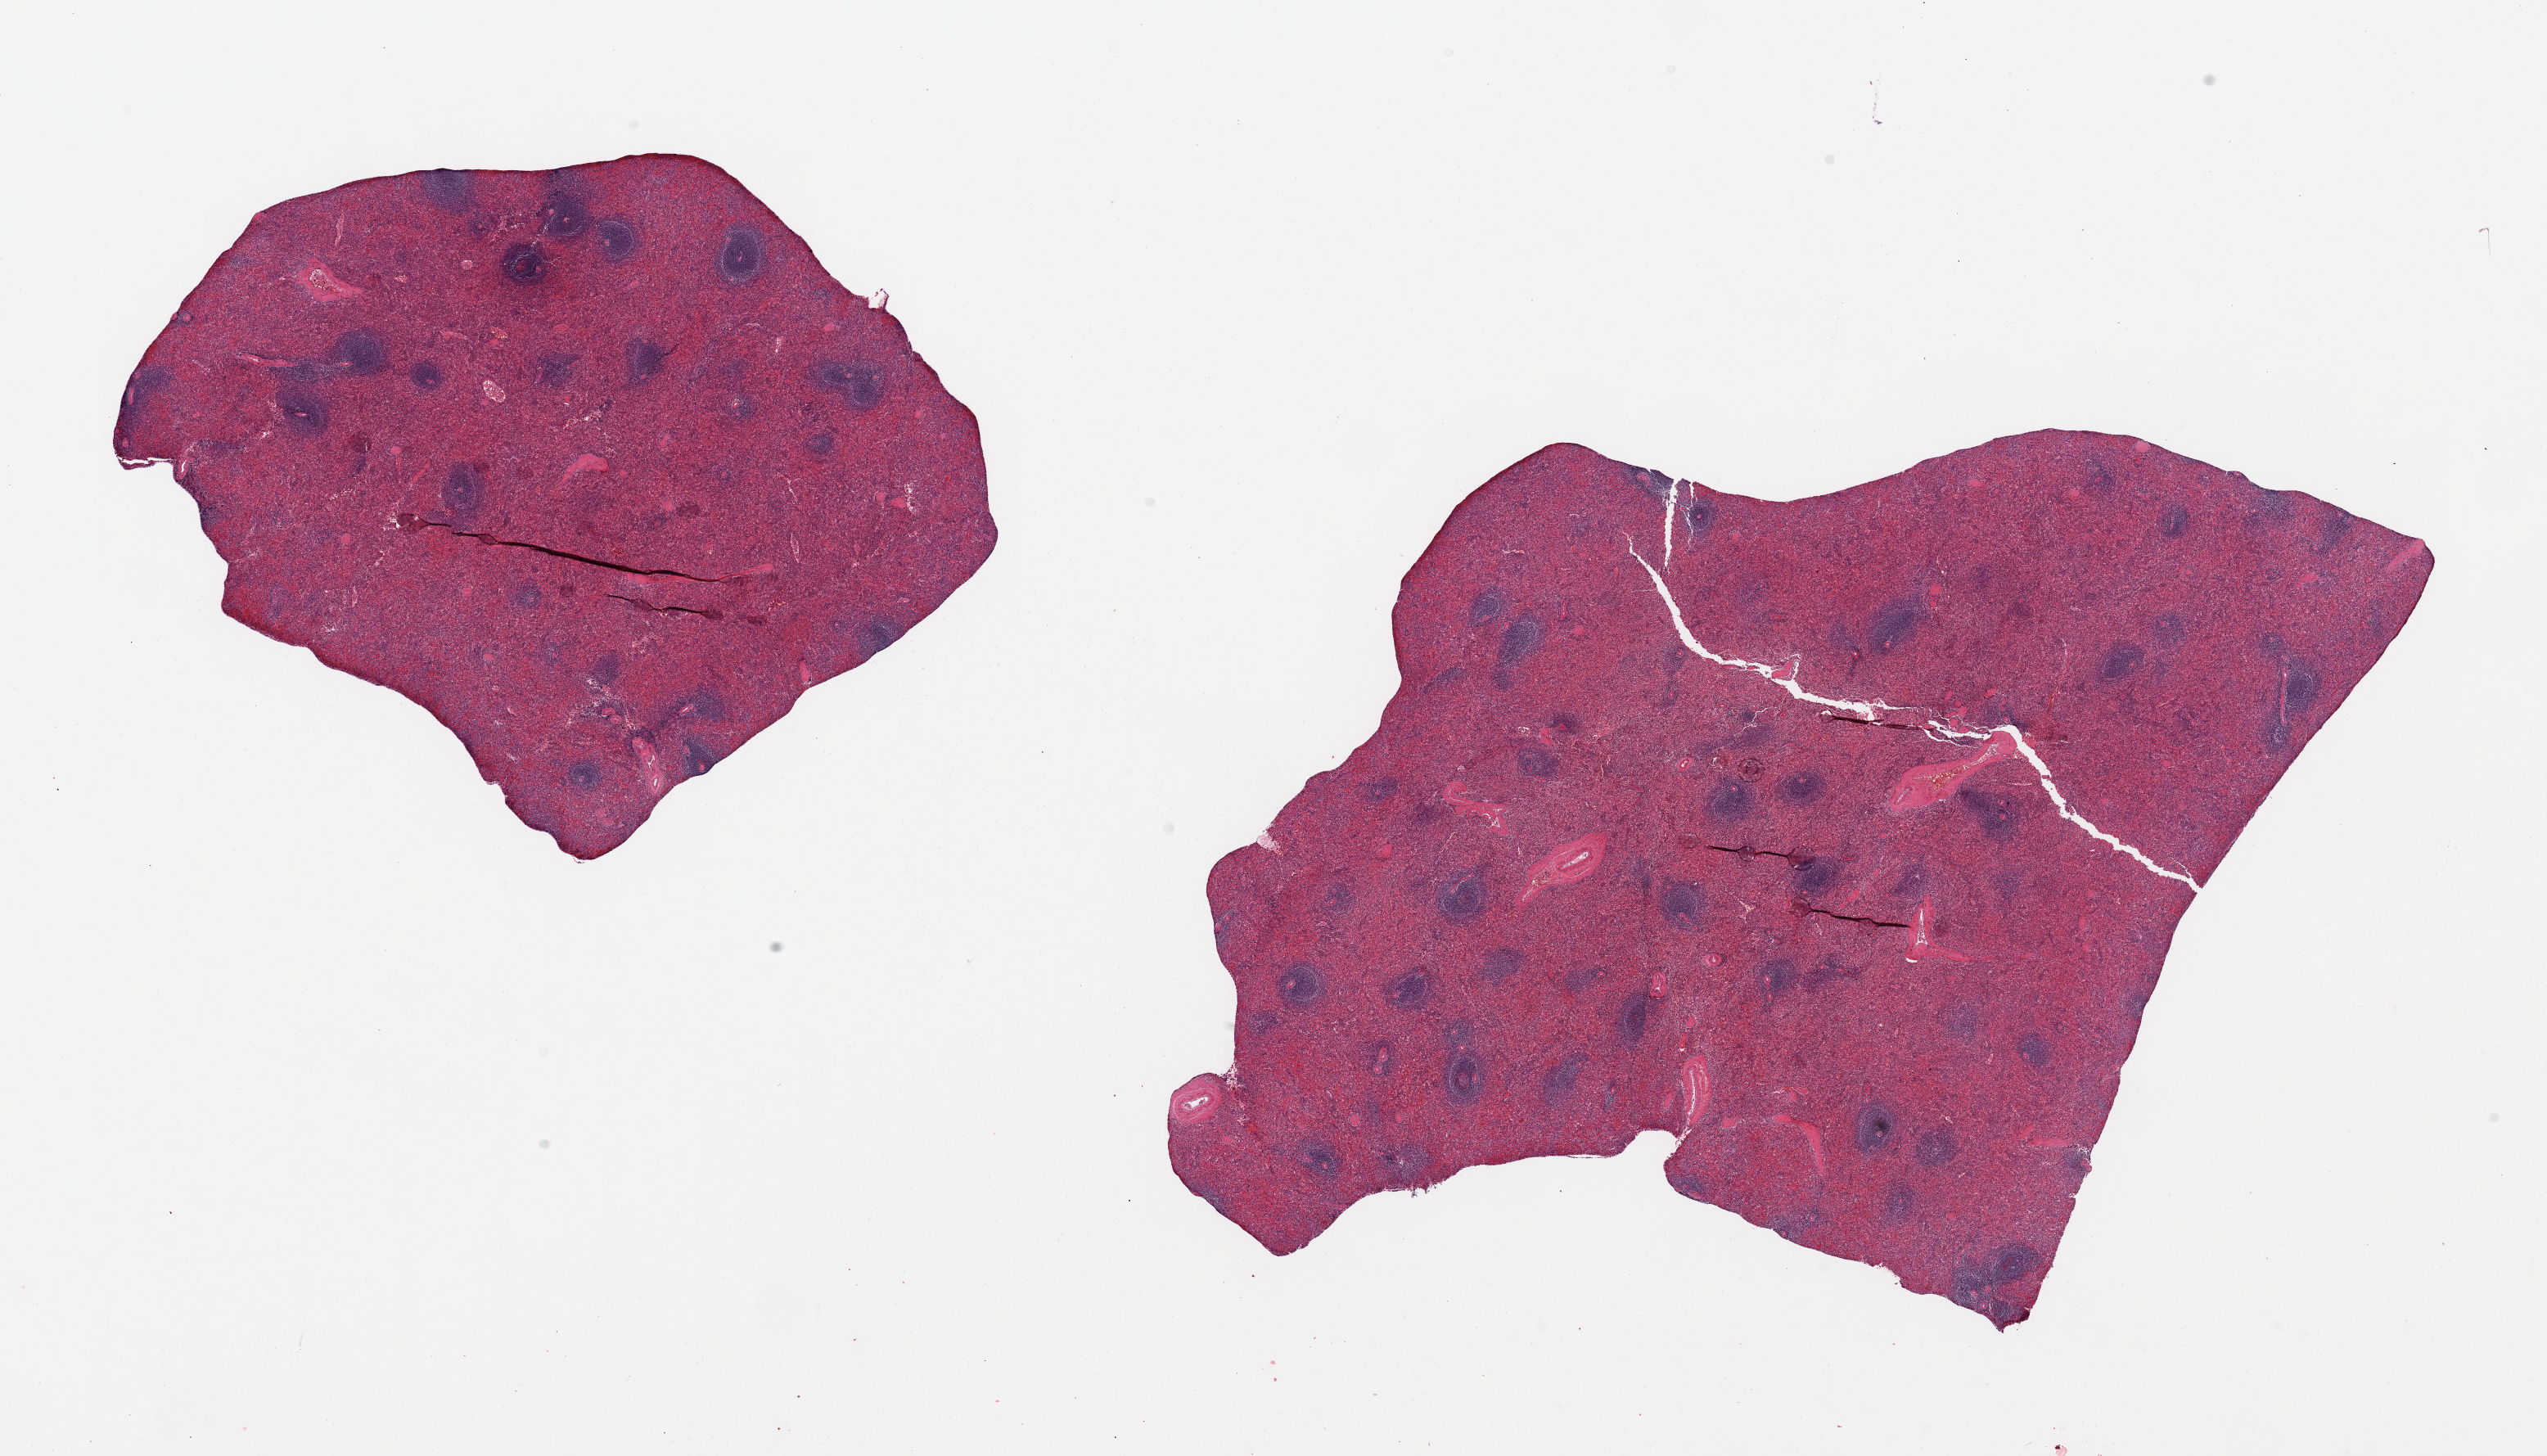
Haematoxylin and eosin whole-slide image, brightfield, low-resolution overview of the scanned area, about 24.6 x 14.1 mm; PAXgene-fixed paraffin-embedded (PFPE) section; sampled site (target tissue): spleen; donor tissue sample.
• reviewer comment on this tissue sample: 2 pieces; mildly congested